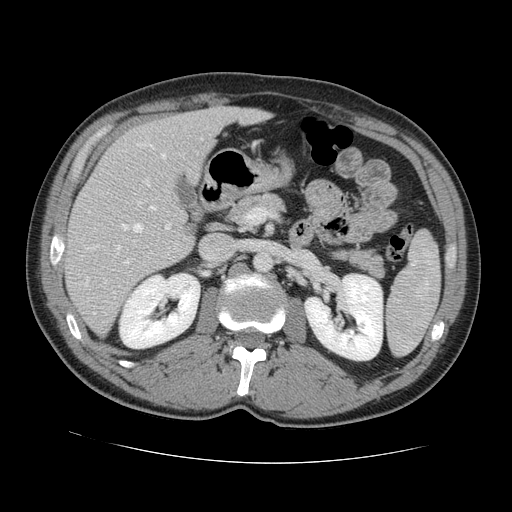
Contrast-enhanced abdominal CT, one axial slice; position 69 of 131 along the scan axis; intravenous contrast given; soft-tissue window (W 400 / L 40 HU); 2.5 mm slice thickness; 512 × 512 image matrix, field of view 380 × 380 mm. Male patient, age 40 years. Case-level facts recorded for this patient, not image findings: diagnosis: colorectal cancer liver metastases, imaged before liver resection; multiple liver metastases: yes; largest metastasis: 2.9 cm; disease in both lobes: yes.
Structures marked on this image (outlined manually by an expert reader):
- hepatic veins: bounding box <86,143,167,285> (left, top, right, bottom; pixels)
- liver: <67,108,265,334>
- planned liver remnant (the part of the liver to remain after resection): <108,108,264,189>
- portal vein (with intrahepatic branches): <124,180,171,264>